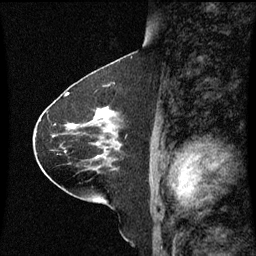
Breast MRI (dynamic contrast-enhanced), one sagittal slice. Slice 35 of 60 in the series (ordered by position). Dynamic contrast-enhanced series, image 2 of 3 at this slice position (ordered by acquisition). 1.5 T. TE 4.2 ms, TR 8.9 ms. 256 × 256 image matrix. Female patient, age 63 years. Case-level facts recorded for this patient, not image findings: setting: breast cancer imaged before/during neoadjuvant chemotherapy; receptor status: HR-positive, HER2-negative.
Outlined on this slice (semi-automatically segmented with operator editing):
- analysis volume of interest (the breast-tissue region the enhancement analysis was run in; not a lesion): box from (x=77, y=106) to (x=123, y=151) px
- tumour enhancement mask (voxels above the 70 % enhancement threshold inside the analysis volume of interest): (x=94, y=110)–(x=112, y=119)